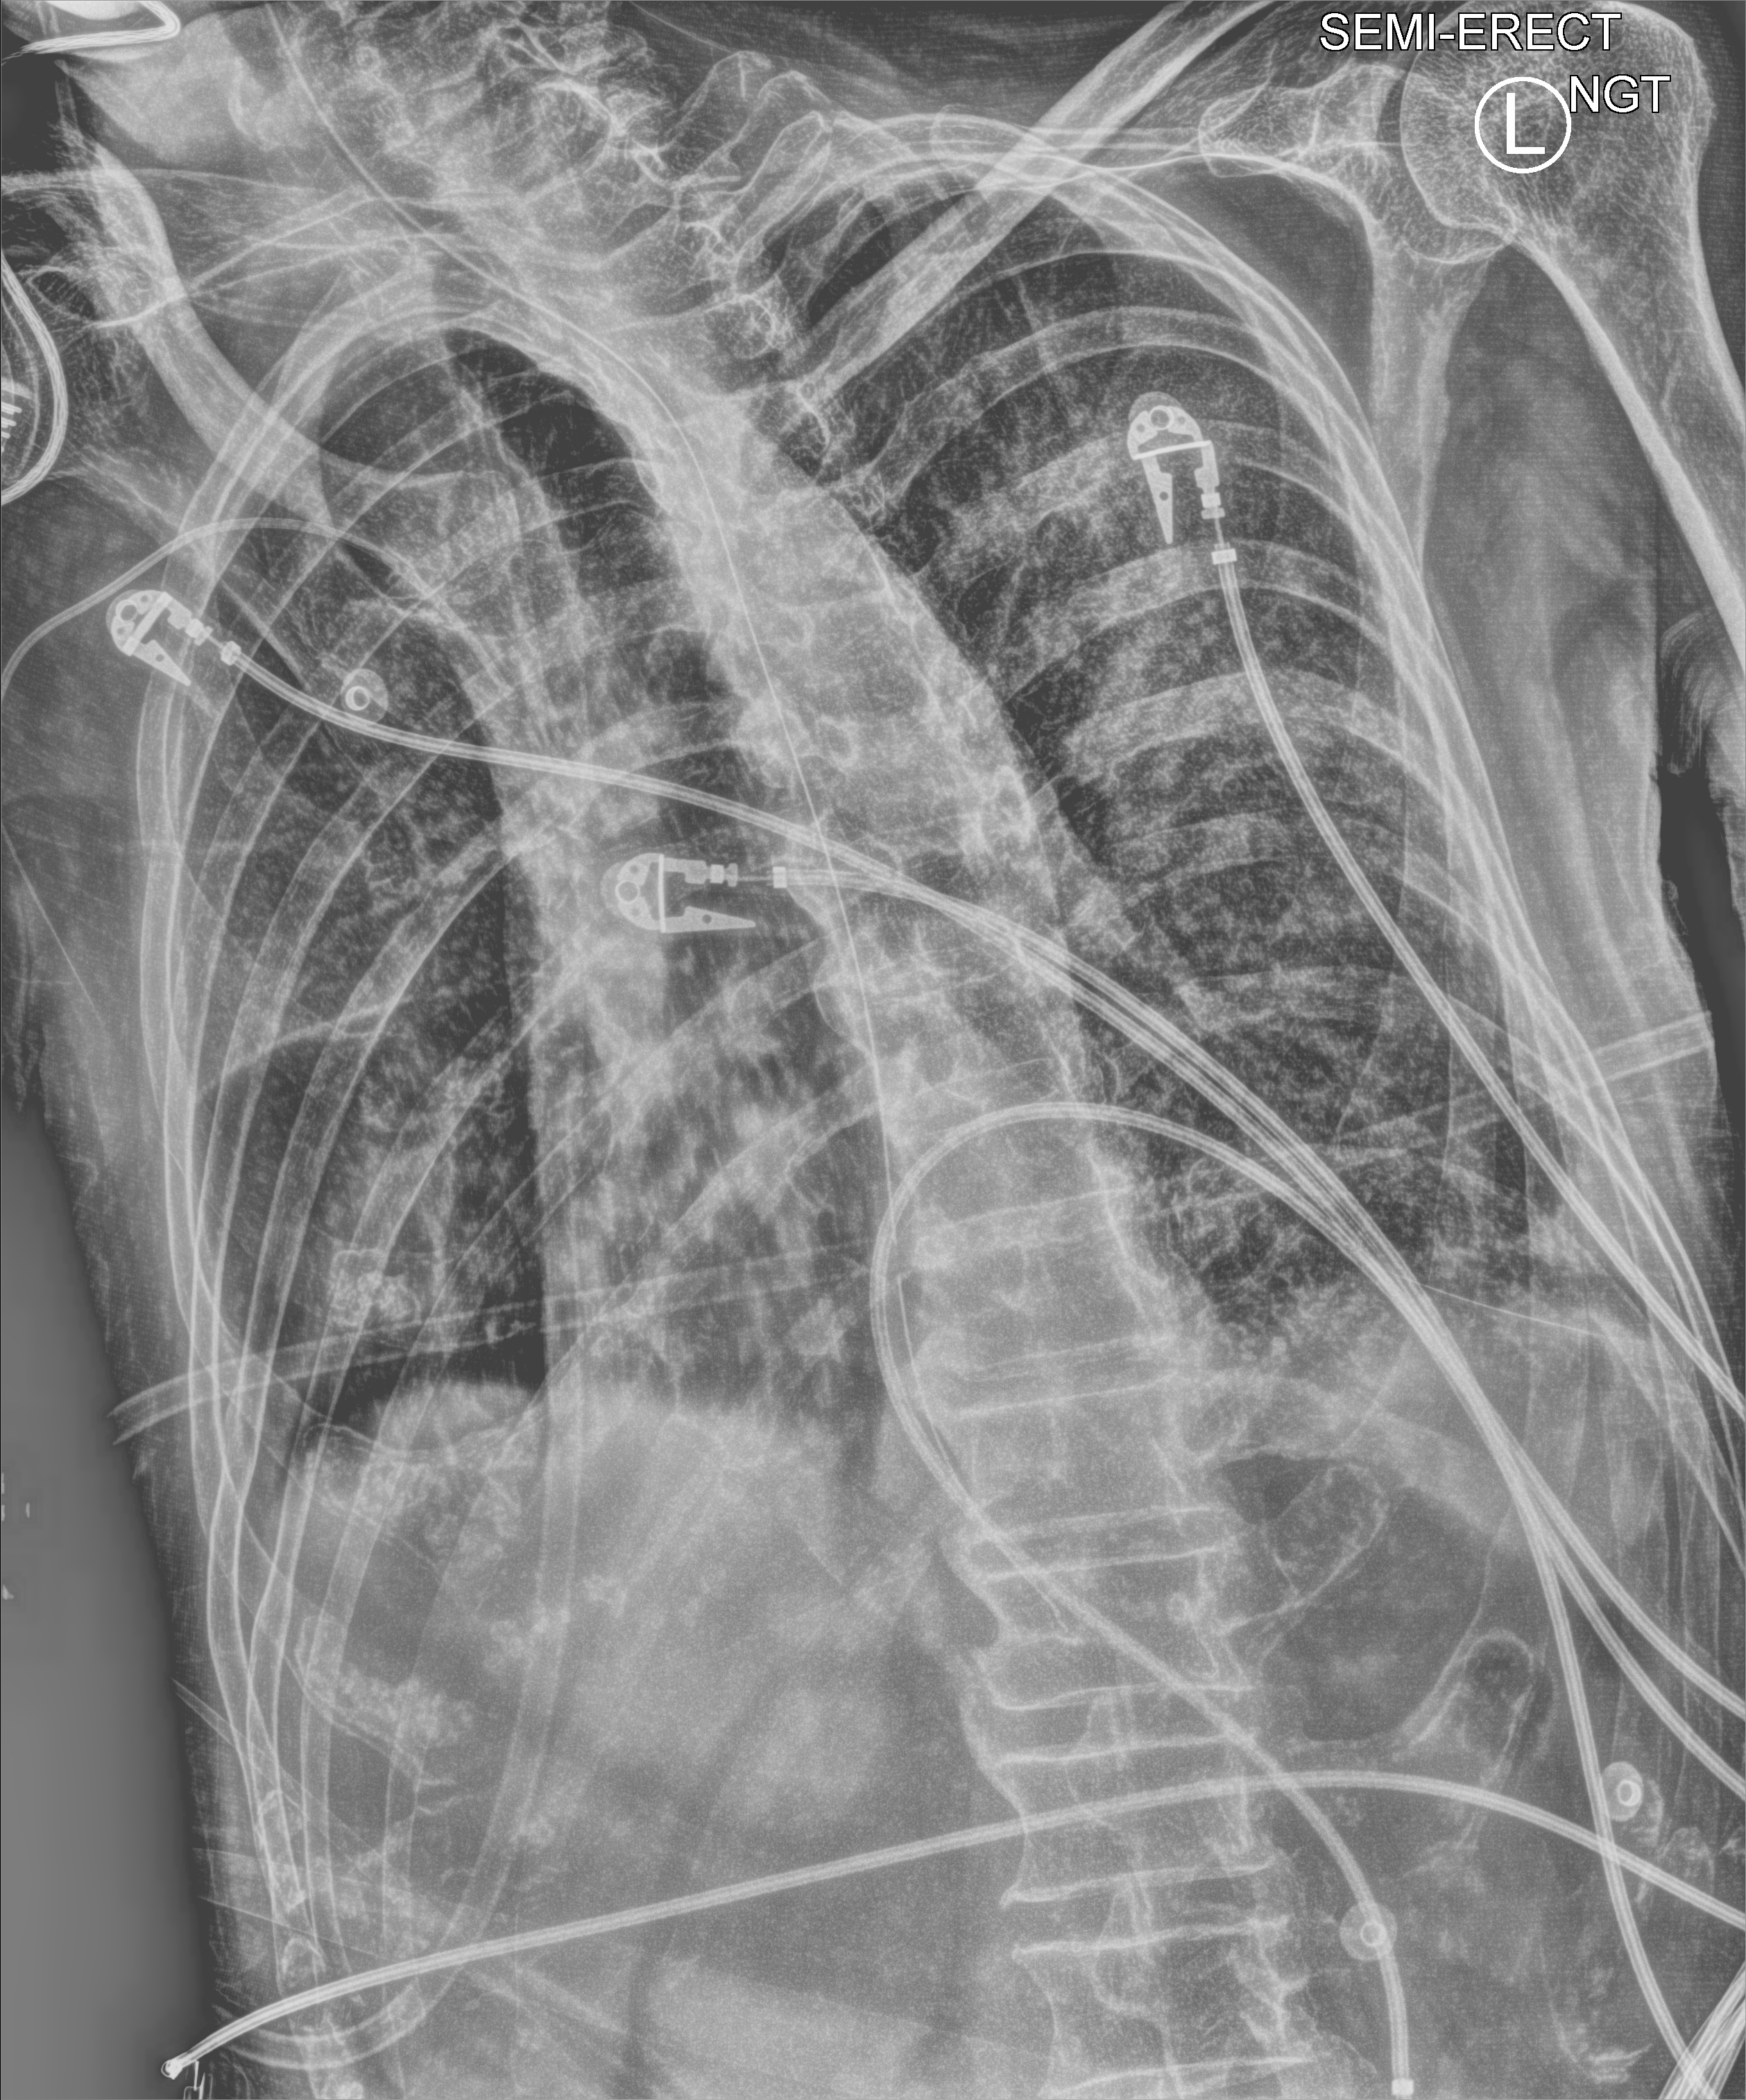
Portable chest radiograph. Patient hospitalised with COVID-19; male, aged 60–74 years.
Hospital-stay facts (about this admission, not read from this image; timing relative to this image not recorded): smoking status (admission record): current; mechanically ventilated during this hospital stay: yes.